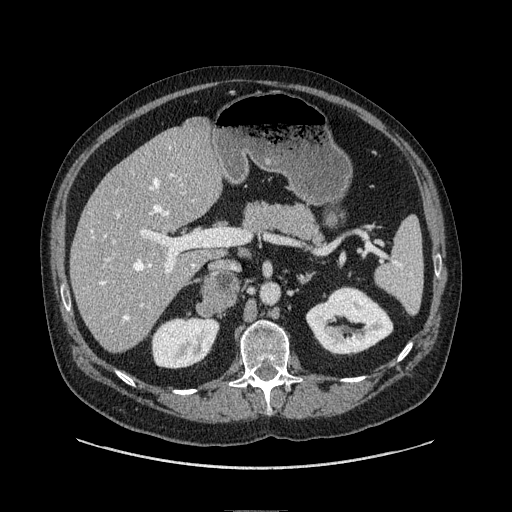
Contrast-enhanced abdominal CT, one axial slice; position 44 of 149 along the scan axis; soft-tissue window (W 400 / L 40 HU); 1.25 mm slice thickness; 512 × 512 image matrix. Male patient. From the clinical record (not read from this slice): diagnosis: adrenocortical carcinoma; tumour side: right adrenal; tumour size at pathology: 7.5 cm; Ki-67 index: 15 %; stage (as recorded): 2.
Outlined on this slice (semi-automatically segmented with operator editing):
- mass: bounding box <199,275,239,313> (left, top, right, bottom; pixels)